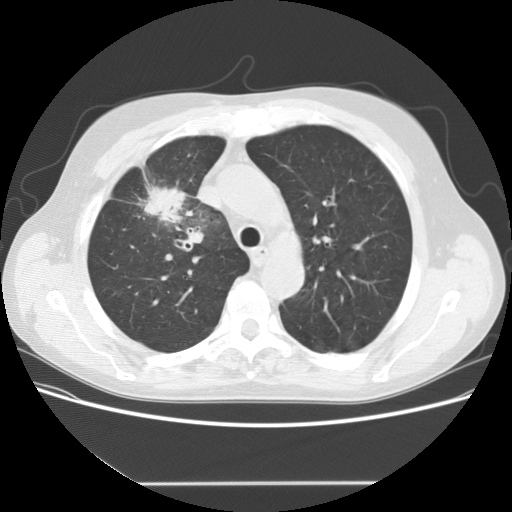
Low-dose screening chest CT, axial slice. Baseline annual screen. Lung window (W 1500 / L -600 HU). 2.5 mm slice thickness. 120 kVp. Slice 42 of 153 in the series. 512 × 512 image matrix. Male participant, aged 56 years at enrolment. Current smoker at enrolment.
• Lesion marked by an expert reader, bounding box (x1, y1, x2, y2) in pixels: (127, 170, 216, 248).
• The screening reader recorded 2 non-calcified nodules or masses ≥4 mm on this exam (right upper lobe, right middle lobe); which of them this box marks is not recorded.